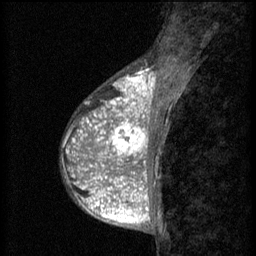
Breast MRI (dynamic contrast-enhanced), one sagittal slice. 3 images stored at this slice position (order not interpretable as contrast timing). 1.5 T. TE 4.2 ms, TR 8.2 ms. 2 mm slice thickness. 256 × 256 image matrix. Female patient, age 38 years.
Structures marked on this image (semi-automatic segmentation, software-assisted and operator-edited):
- analysis volume of interest (the breast-tissue region the enhancement analysis was run in; not a lesion): box from (x=92, y=112) to (x=152, y=171) px
- tumour enhancement mask (voxels above the 70 % enhancement threshold inside the analysis volume of interest): (x=92, y=112)–(x=150, y=171)